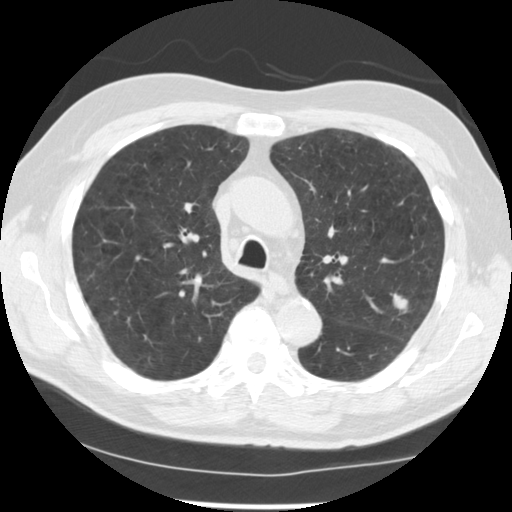
Axial slice from a low-dose chest CT screening exam; baseline screening round; lung window (W 1500 / L -600 HU); 120 kVp; slice 169 of 249 in the series. Male participant, aged 71 years at enrolment. Current smoker at enrolment.
- Lesion marked by an expert reader, bounding box (x1, y1, x2, y2) in pixels: (382, 283, 424, 328).
- The screening reader recorded 2 non-calcified nodules or masses ≥4 mm on this exam (left upper lobe, left upper lobe); which of them this box marks is not recorded.
- Official screen result: positive, change unspecified: nodule(s) >= 4 mm or enlarging nodule(s), mass(es), or other non-specific abnormalities suspicious for lung cancer.
- Lung cancer was diagnosed 37 days after this screen: adenocarcinoma, NOS, left upper lobe, poorly differentiated (G3), stage IIIB (AJCC 6th edition), 25 mm at pathology.